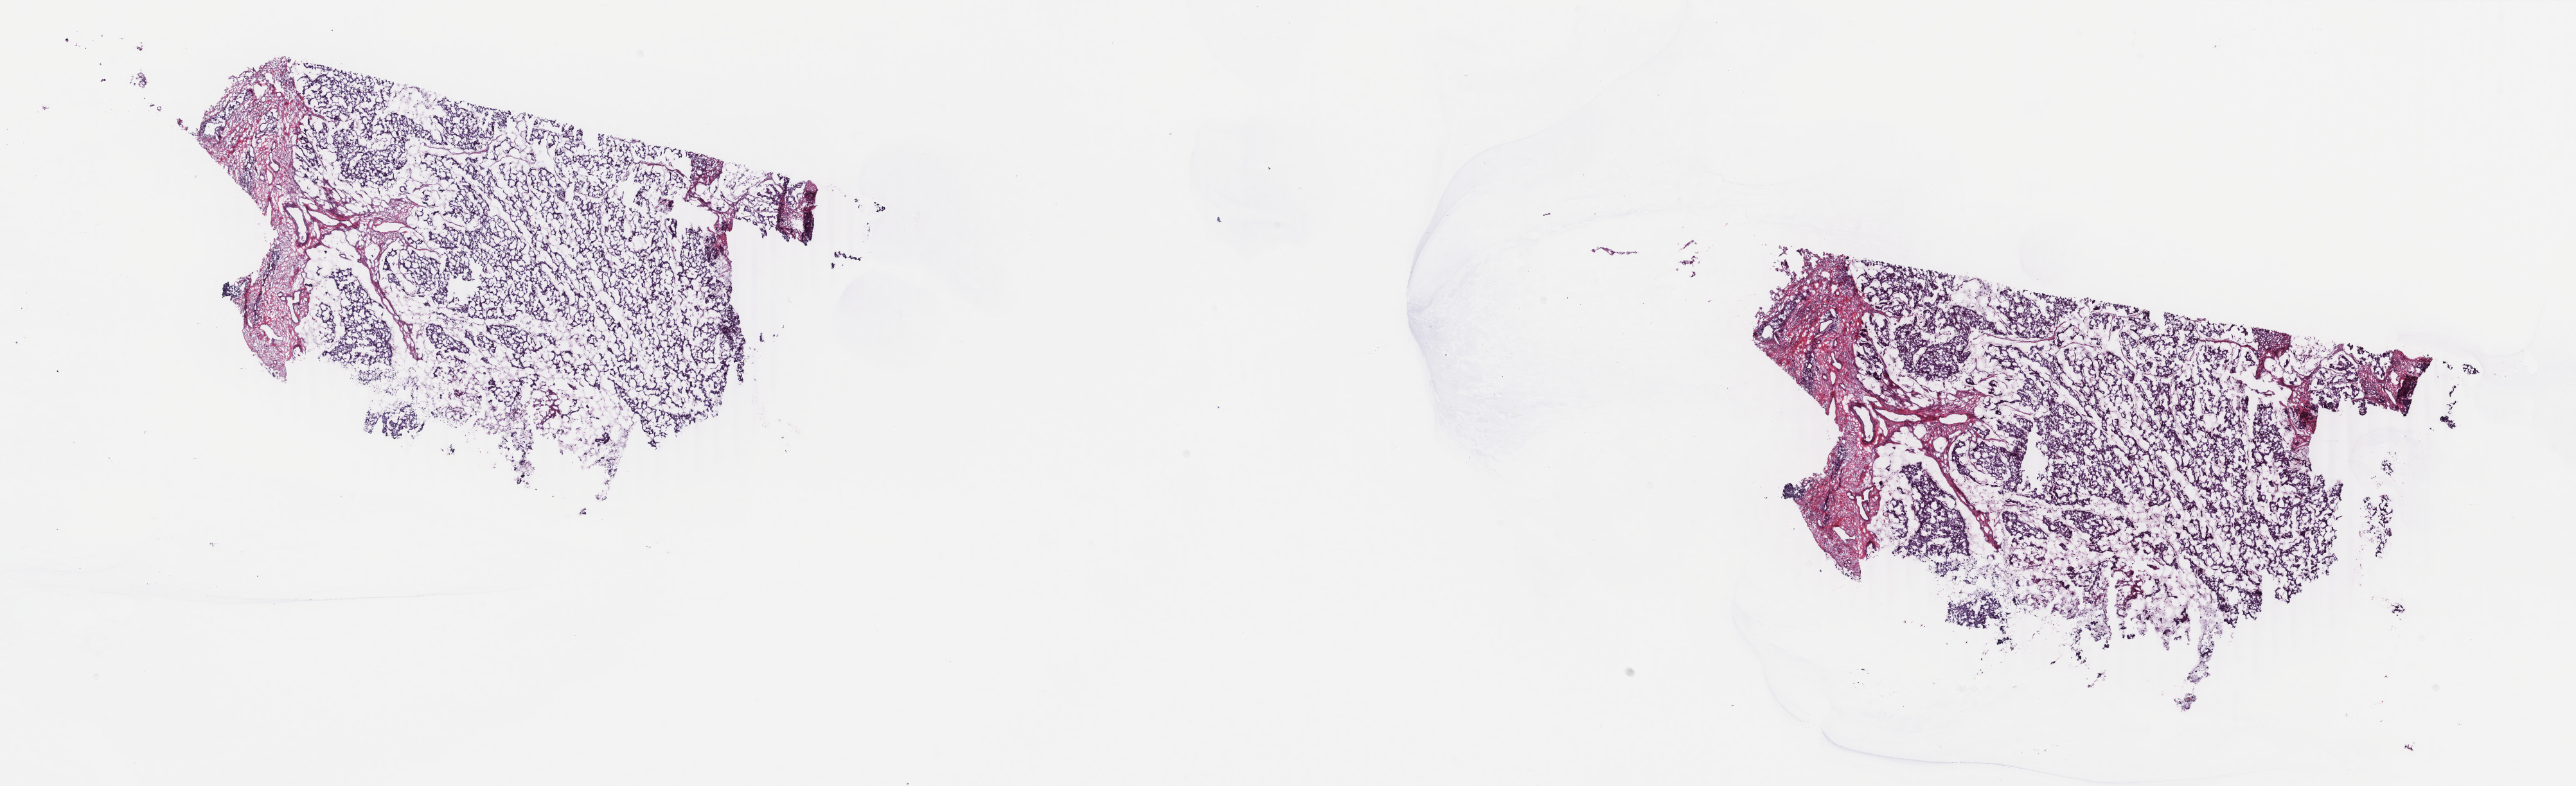
Digitized Hematoxylin and eosin (H&E) stained tissue section (whole slide) — whole scanned area (about 31.9 x 9.7 mm) shown as a low-resolution overview; frozen section; breast, primary tumour sample. Patient: female, age at initial diagnosis 69 years. Pathologist review of this section (percent, as recorded): tumour cells 90%, tumour nuclei 90%.
Histologic diagnosis: Infiltrating duct mixed with other types of carcinoma.